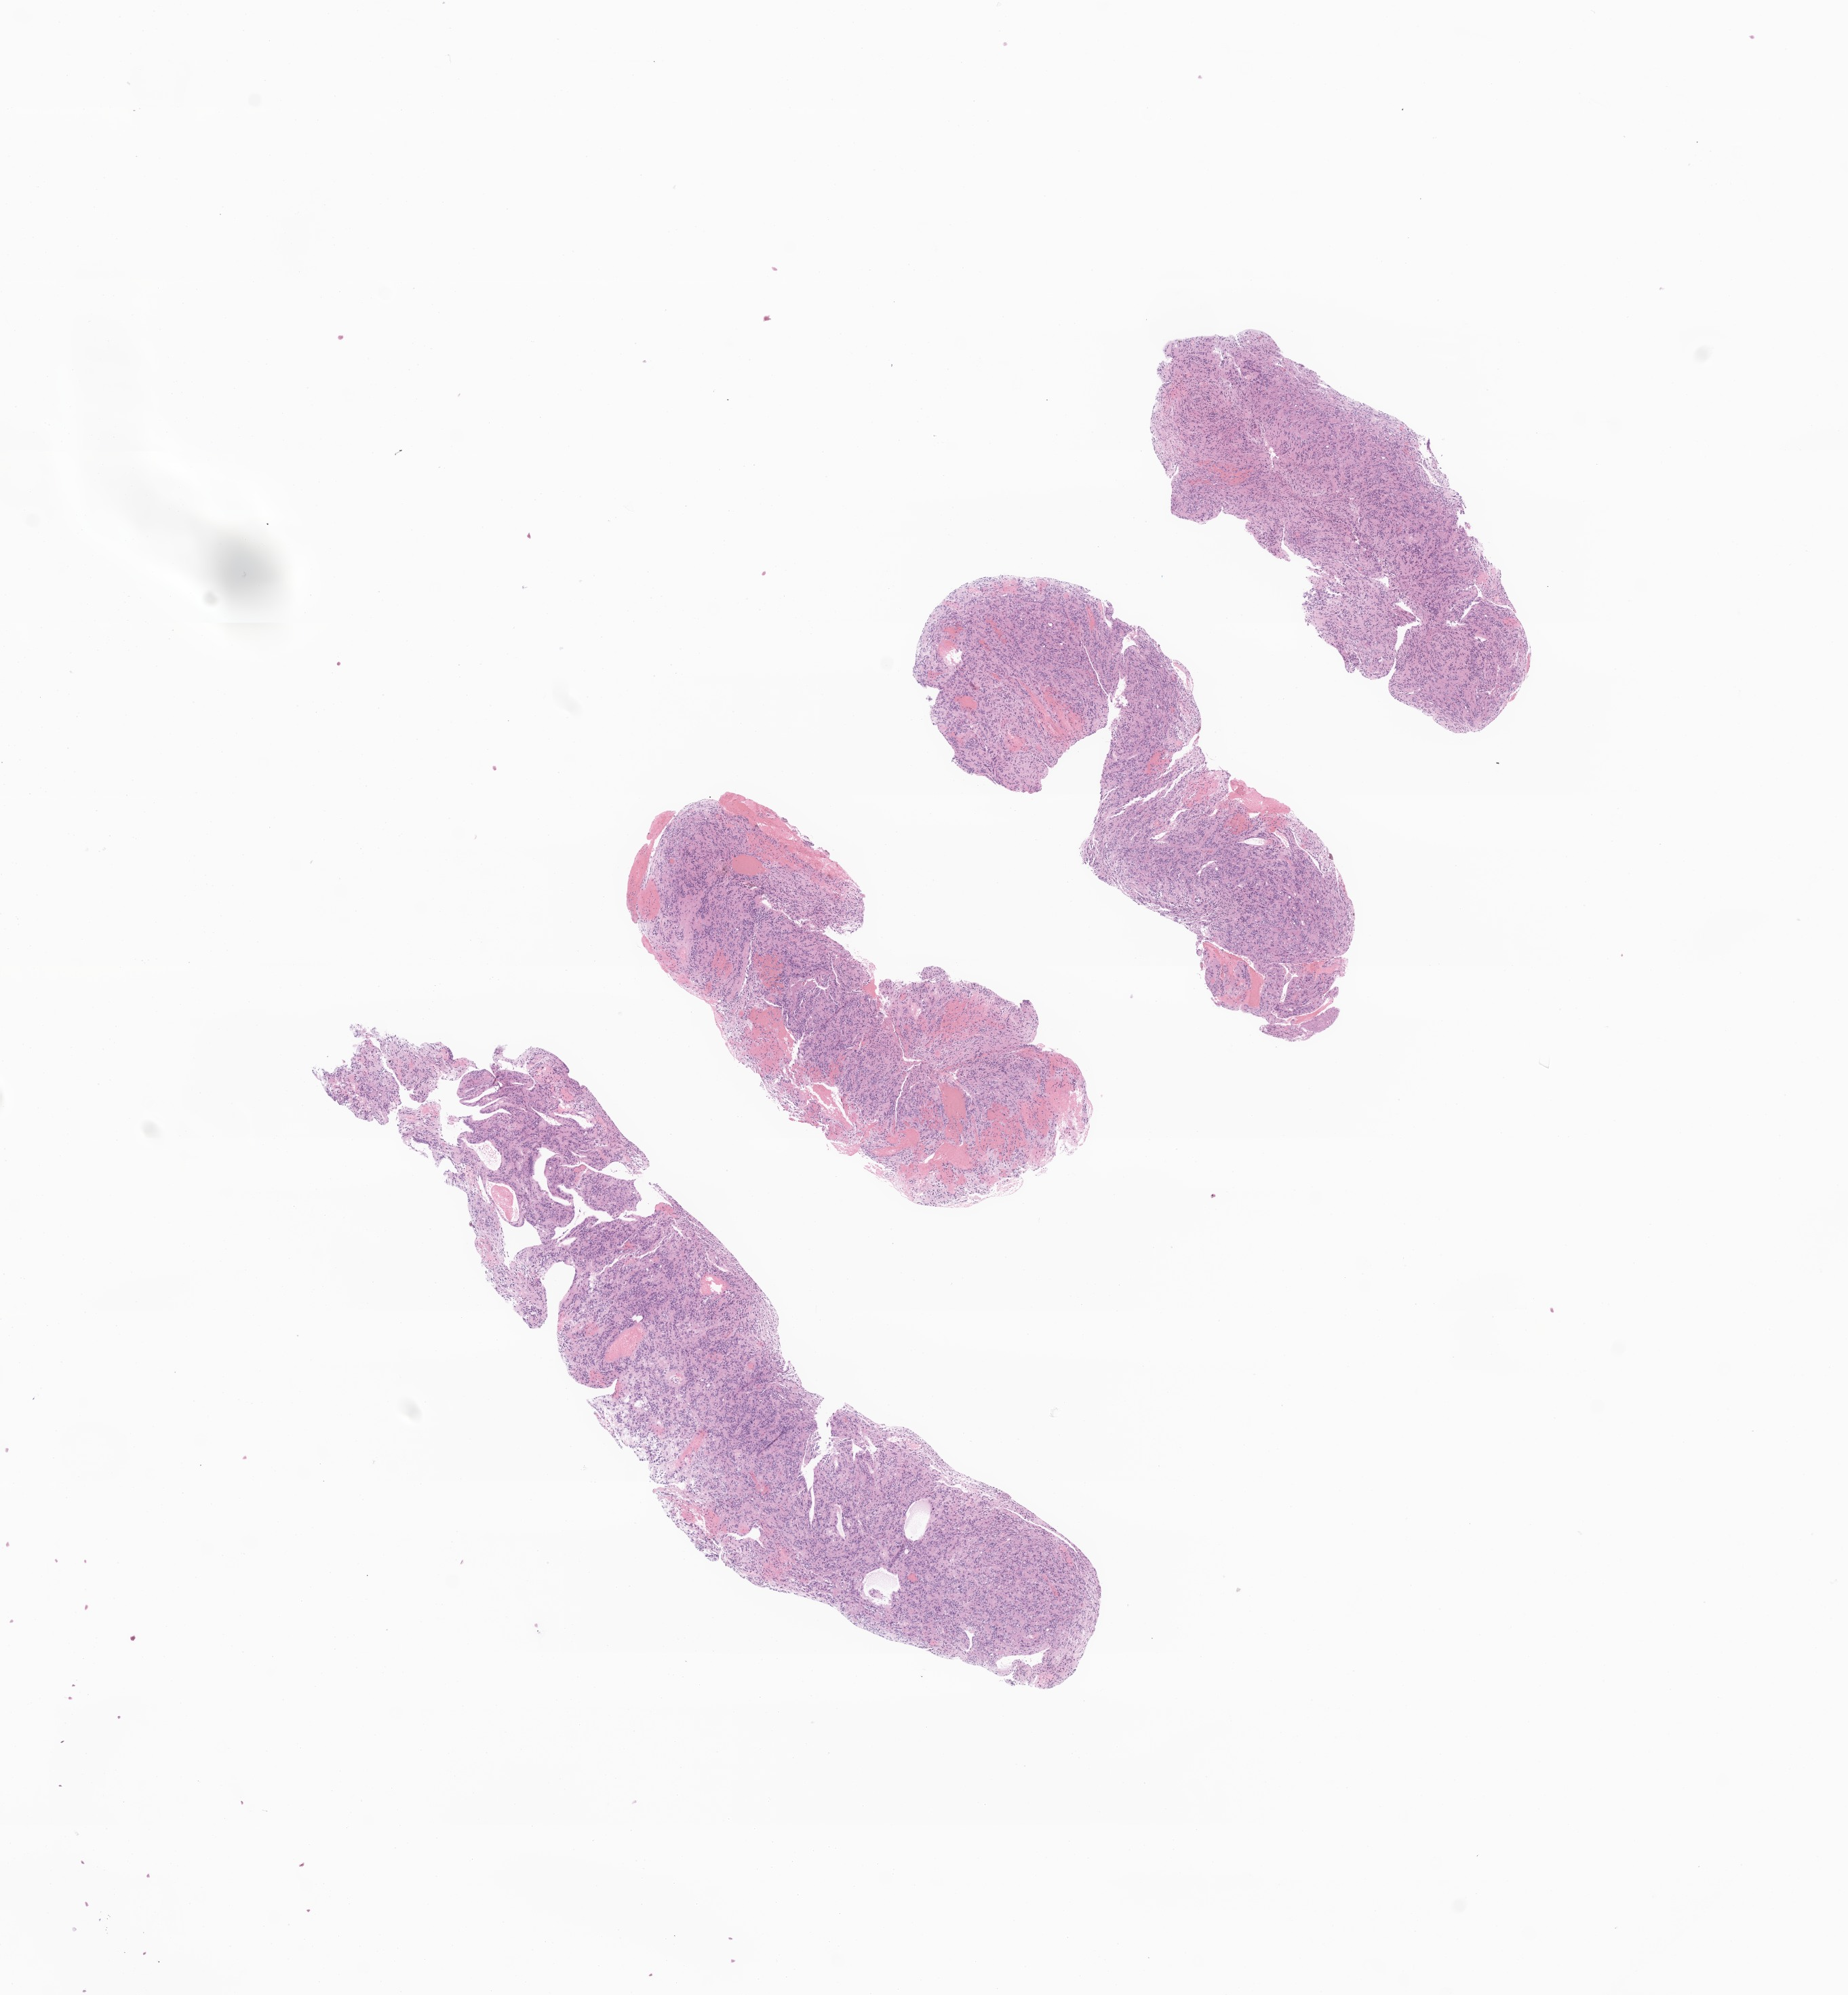
H&E whole-slide image of tumor tissue from the brain — low-resolution overview of the scanned area, about 11.5 x 12.4 mm, FFPE section. Male patient, age 216 months.
Diagnosis (ICD-O-3 morphology term): Glioma, malignant.